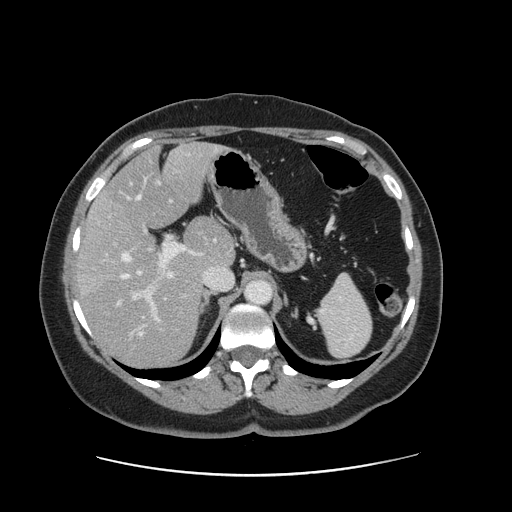
Contrast-enhanced abdominal CT, one axial slice. Slice 95 of 161 in the series (ordered by position). Intravenous contrast given. Soft-tissue window (W 400 / L 40 HU). 2.5 mm slice thickness. 512 × 512 image matrix. Female patient, age 62 years. From the clinical record (not read from this slice): diagnosis: colorectal cancer liver metastases, imaged before liver resection; multiple liver metastases: no; largest metastasis: 2.5 cm; disease in both lobes: no.
Annotated regions visible in this slice (manually delineated by an expert):
- hepatic veins: box from (x=119, y=178) to (x=147, y=335) px
- liver: (x=80, y=144)–(x=234, y=366)
- planned liver remnant (the part of the liver to remain after resection): (x=104, y=144)–(x=234, y=268)
- portal vein (with intrahepatic branches): (x=129, y=236)–(x=193, y=339)